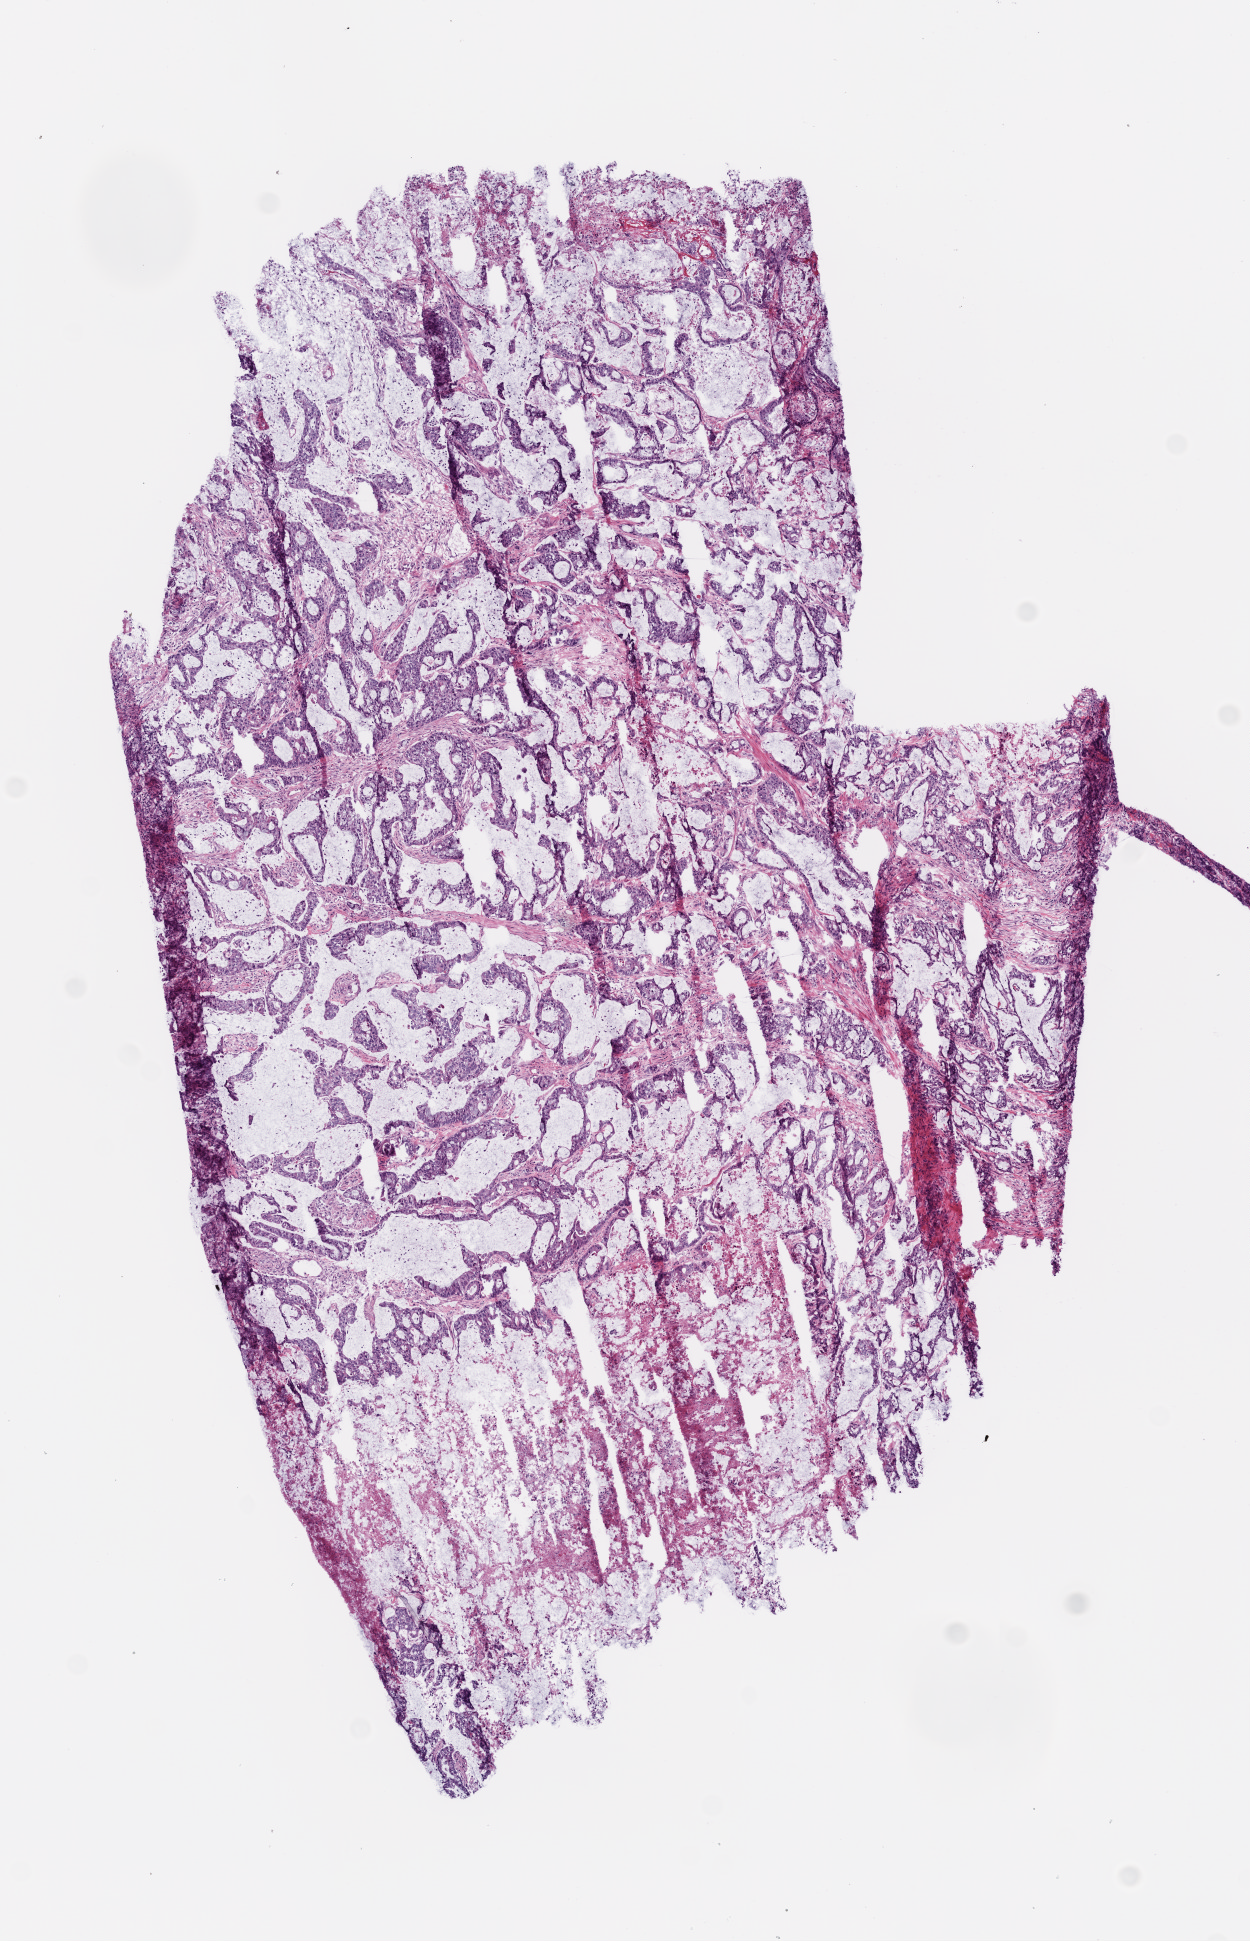
Whole-slide histology image, H&E — whole scanned area (about 5.0 x 7.8 mm, from a 20x scan) shown as a low-resolution overview, frozen section, primary tumour sample from the colon. Male patient; age at initial diagnosis 71 years.
Diagnosis: Mucinous adenocarcinoma (sigmoid colon).